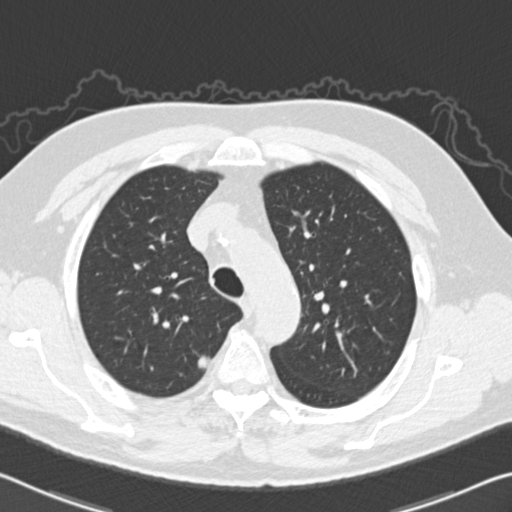
Axial slice from a low-dose chest CT screening exam, baseline annual screen, lung window (W 1500 / L -600 HU), 2 mm slice thickness, standard (soft-tissue) reconstruction kernel (B30f), 512 × 512 image matrix. Male participant, aged 64 years at enrolment. Former smoker at enrolment.
Expert-annotated lung lesion, box from (x=184, y=344) to (x=228, y=384) px. Screening reader's record for this exam (one nodule recorded; not confirmed to be the boxed lesion): non-calcified nodule or mass ≥4 mm, right upper lobe, 10 × 8 mm, spiculated (stellate) margins, soft tissue attenuation.